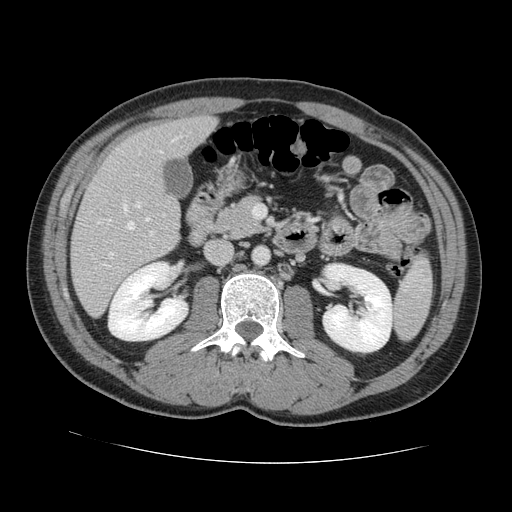
Contrast-enhanced abdominal CT, one axial slice; slice 57 of 131 in the series (ordered by position); 120 kVp; intravenous contrast given; soft-tissue window (W 400 / L 40 HU); 2.5 mm slice thickness; 512 × 512 image matrix, field of view 380 × 380 mm. Male patient, age 40 years. From the clinical record (not read from this slice): diagnosis: colorectal cancer liver metastases, imaged before liver resection; multiple liver metastases: yes; largest metastasis: 2.9 cm; disease in both lobes: yes.
Annotated regions visible in this slice (expert manual segmentation):
- hepatic veins: bounding box (x1, y1, x2, y2) in pixels: (108, 136, 181, 257)
- liver: (72, 117, 214, 314)
- planned liver remnant (the part of the liver to remain after resection): (113, 118, 215, 174)
- portal vein (with intrahepatic branches): (104, 202, 154, 267)